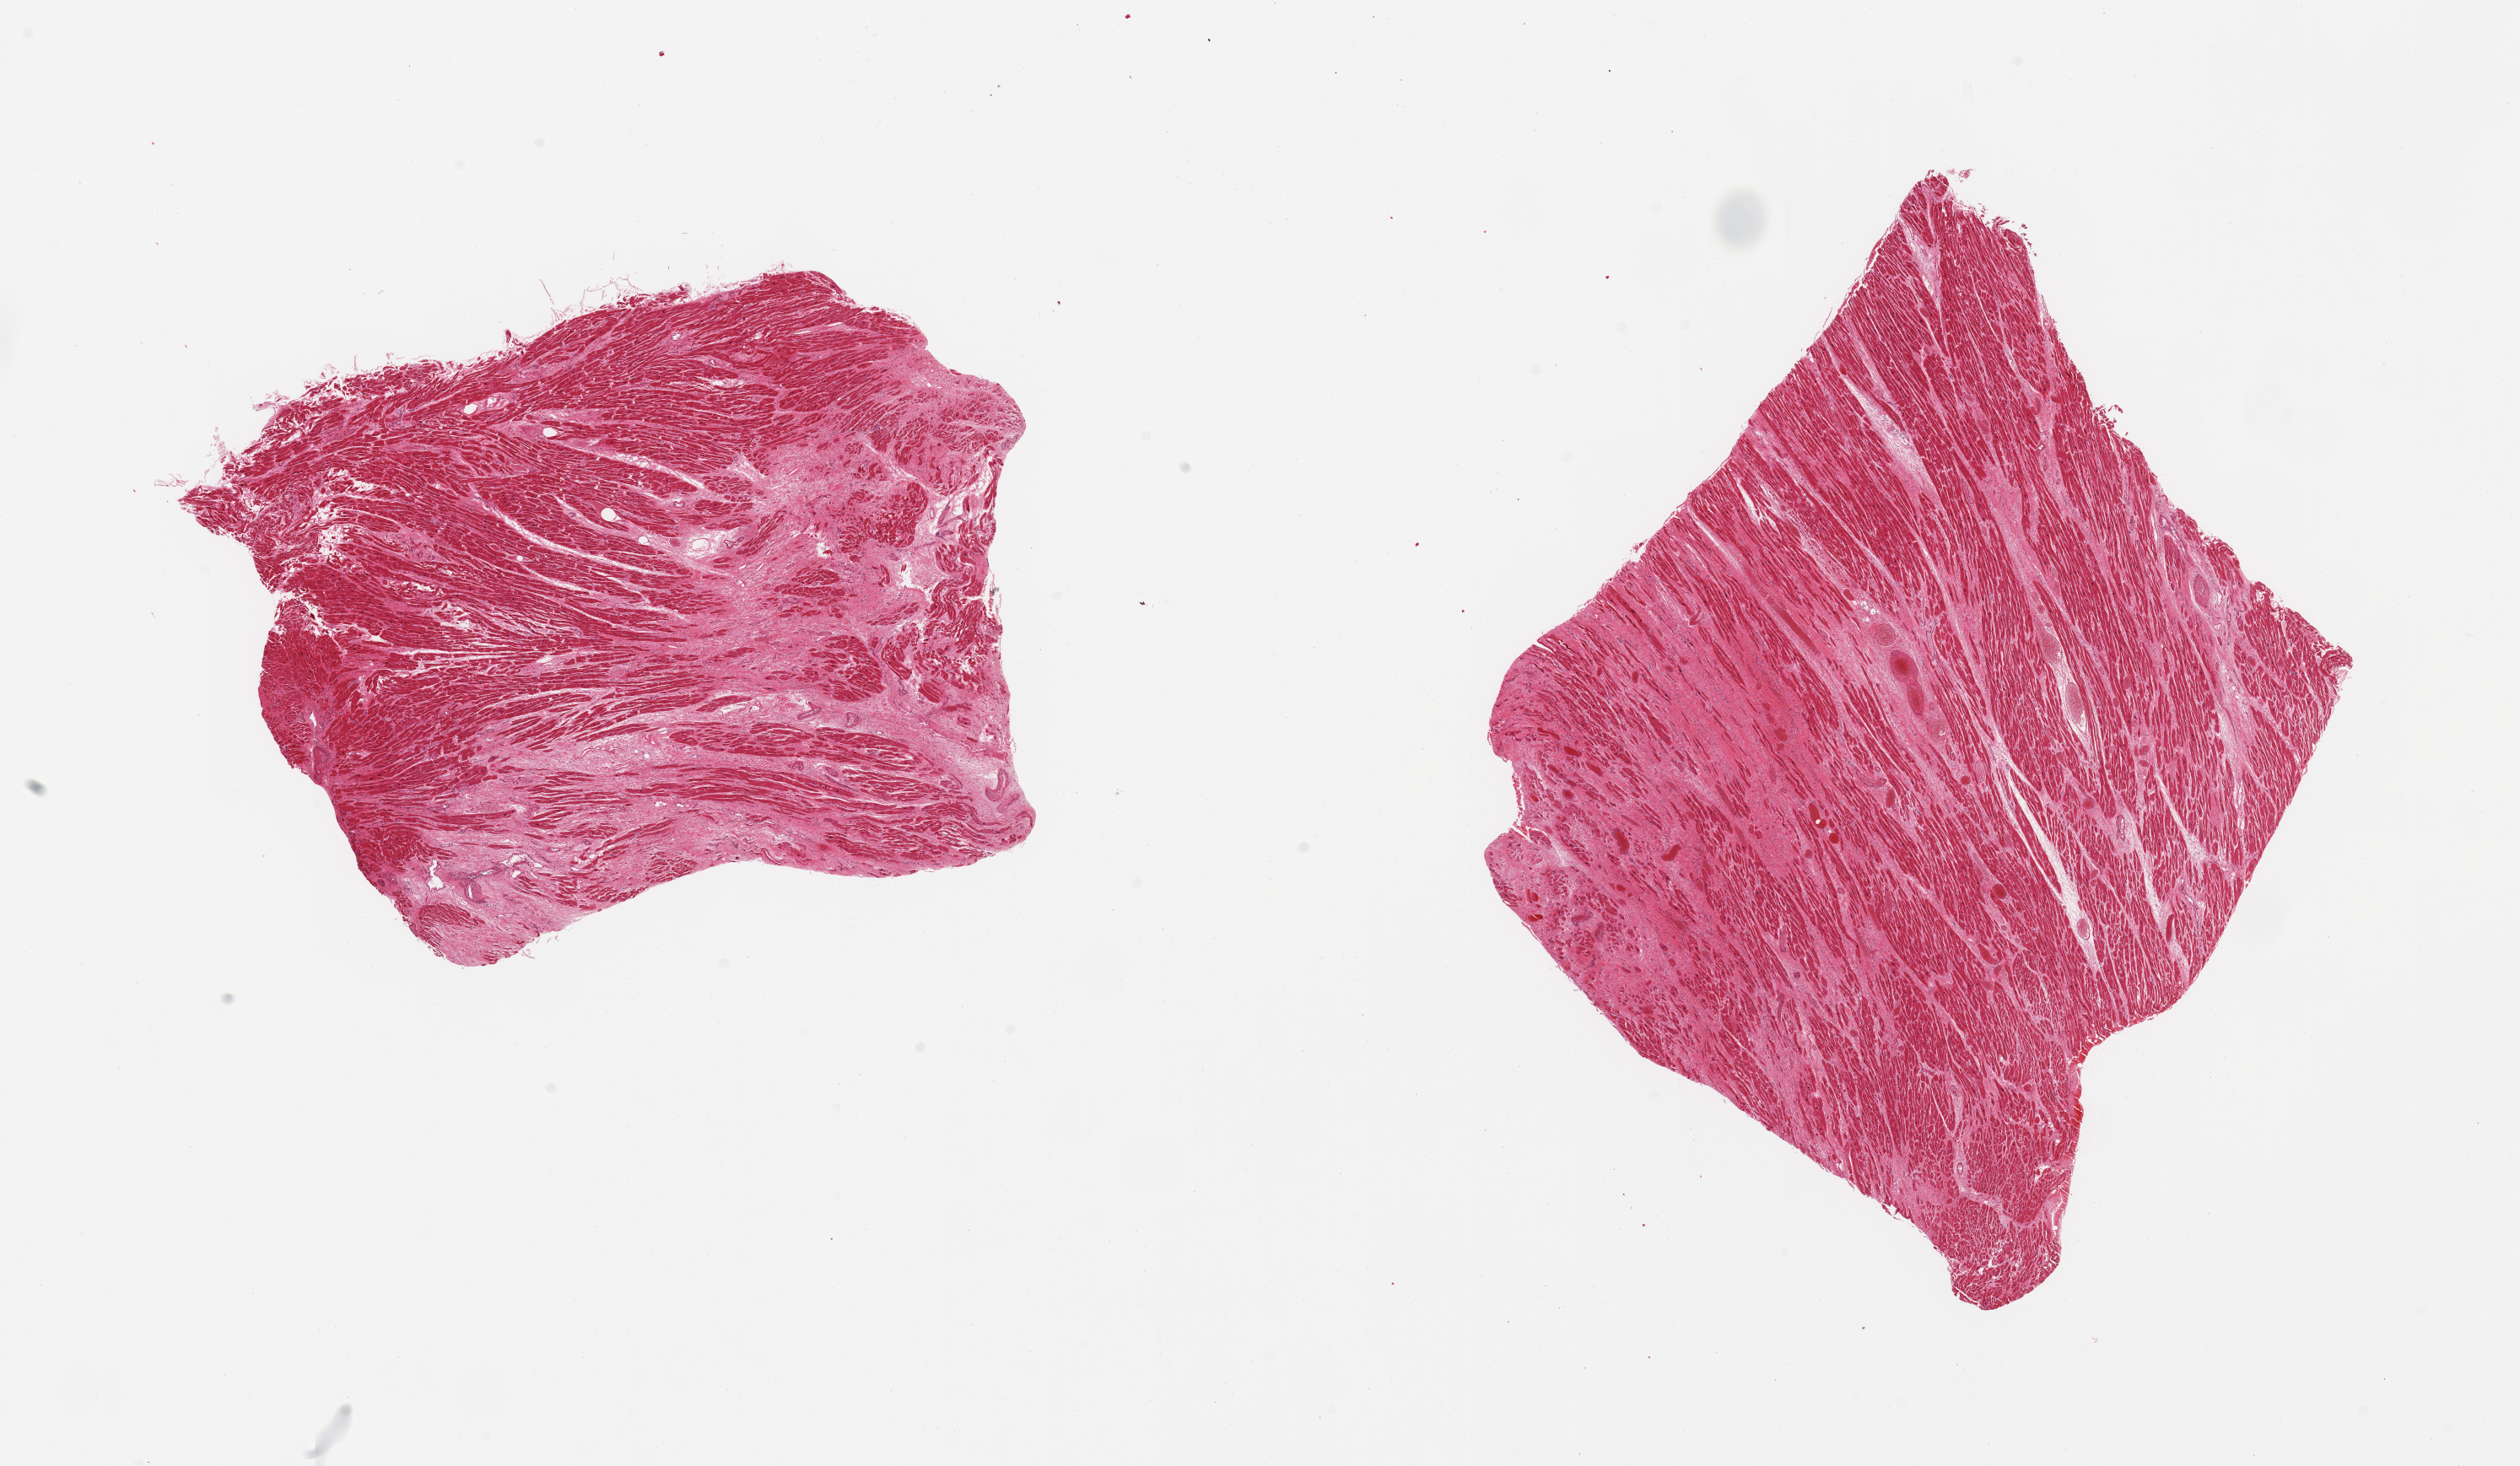
Whole-slide image, H&E stain — shown as a low-resolution overview of the whole scanned area (about 23.6 x 13.7 mm). PAXgene-fixed, paraffin-embedded tissue. Sampled site (target tissue): heart. Donor tissue sample. Donor sex: male.
Review note (as recorded): 2 pieces, healed remote infarcts up to 5x3mm.